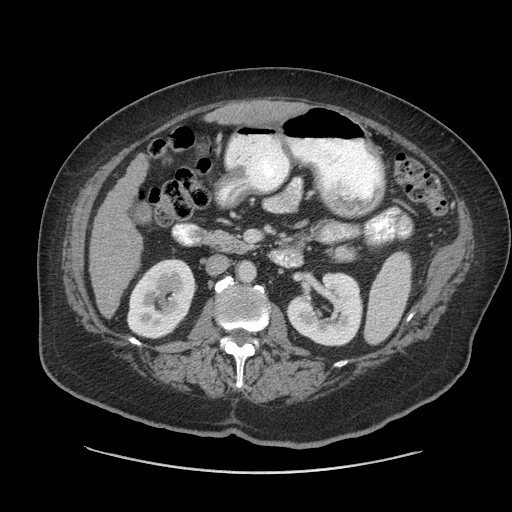
Contrast-enhanced abdominal CT (liver protocol), one axial slice; position 21 of 91 along the scan axis; reconstruction kernel STANDARD; soft-tissue window (W 400 / L 40 HU); 512 × 512 image matrix, field of view 420 × 420 mm. From the clinical record (not read from this slice): diagnosis: hepatocellular carcinoma (patient treated with transarterial chemoembolisation; whether this scan precedes or follows treatment is not stated here); TNM stage (as recorded): Stage-I; Child-Pugh class: A; tumour nodularity: uninodular.
Outlined on this slice (semi-automatically segmented with operator editing):
- liver parenchyma outside the tumour (the mass and vessels are separate outlines, so this box may not span the whole liver): box from (x=90, y=154) to (x=148, y=316) px